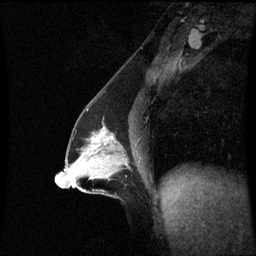
Breast MRI (dynamic contrast-enhanced), one sagittal slice; position 34 of 60 along the scan axis; dynamic contrast-enhanced series, image 2 of 3 at this slice position (ordered by acquisition); 1.5 T; TE 4.2 ms, TR 8.9 ms; 256 × 256 image matrix, field of view 210 × 210 mm. Patient: female, 47 years. From the clinical record (not read from this slice): setting: breast cancer imaged before/during neoadjuvant chemotherapy; receptor status: HR-positive, HER2-negative.
Outlined on this slice (semi-automatically segmented with operator editing):
- analysis volume of interest (the breast-tissue region the enhancement analysis was run in; not a lesion): bounding box [x1, y1, x2, y2] px = [64, 118, 132, 196]
- tumour enhancement mask (voxels above the 70 % enhancement threshold inside the analysis volume of interest): [94, 132, 116, 150]